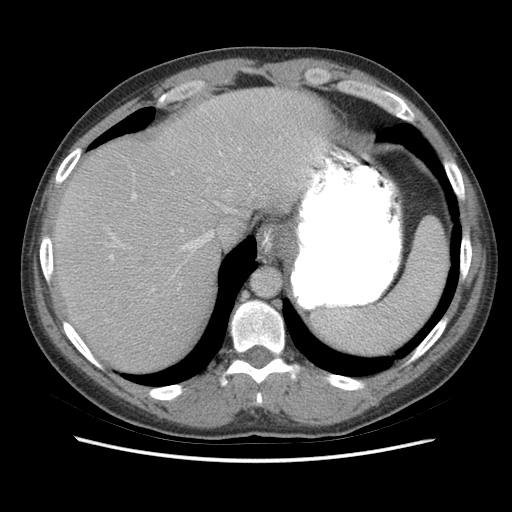
Contrast-enhanced abdominal CT (liver protocol), one axial slice; position 57 of 73 along the scan axis; 140 kVp; soft-tissue window (W 400 / L 40 HU); 2.5 mm slice thickness; 512 × 512 image matrix, field of view 360 × 360 mm. Case-level facts recorded for this patient, not image findings: diagnosis: hepatocellular carcinoma (patient treated with transarterial chemoembolisation; whether this scan precedes or follows treatment is not stated here); TNM stage (as recorded): Stage-IIIA; Child-Pugh class: A; tumour nodularity: multinodular.
Structures marked on this image (semi-automatic segmentation, software-assisted and operator-edited):
- abdominal aorta: bounding box [x1, y1, x2, y2] px = [252, 268, 281, 295]
- liver parenchyma outside the tumour (the mass and vessels are separate outlines, so this box may not span the whole liver): [52, 86, 328, 372]
- liver vessels: [110, 143, 324, 260]